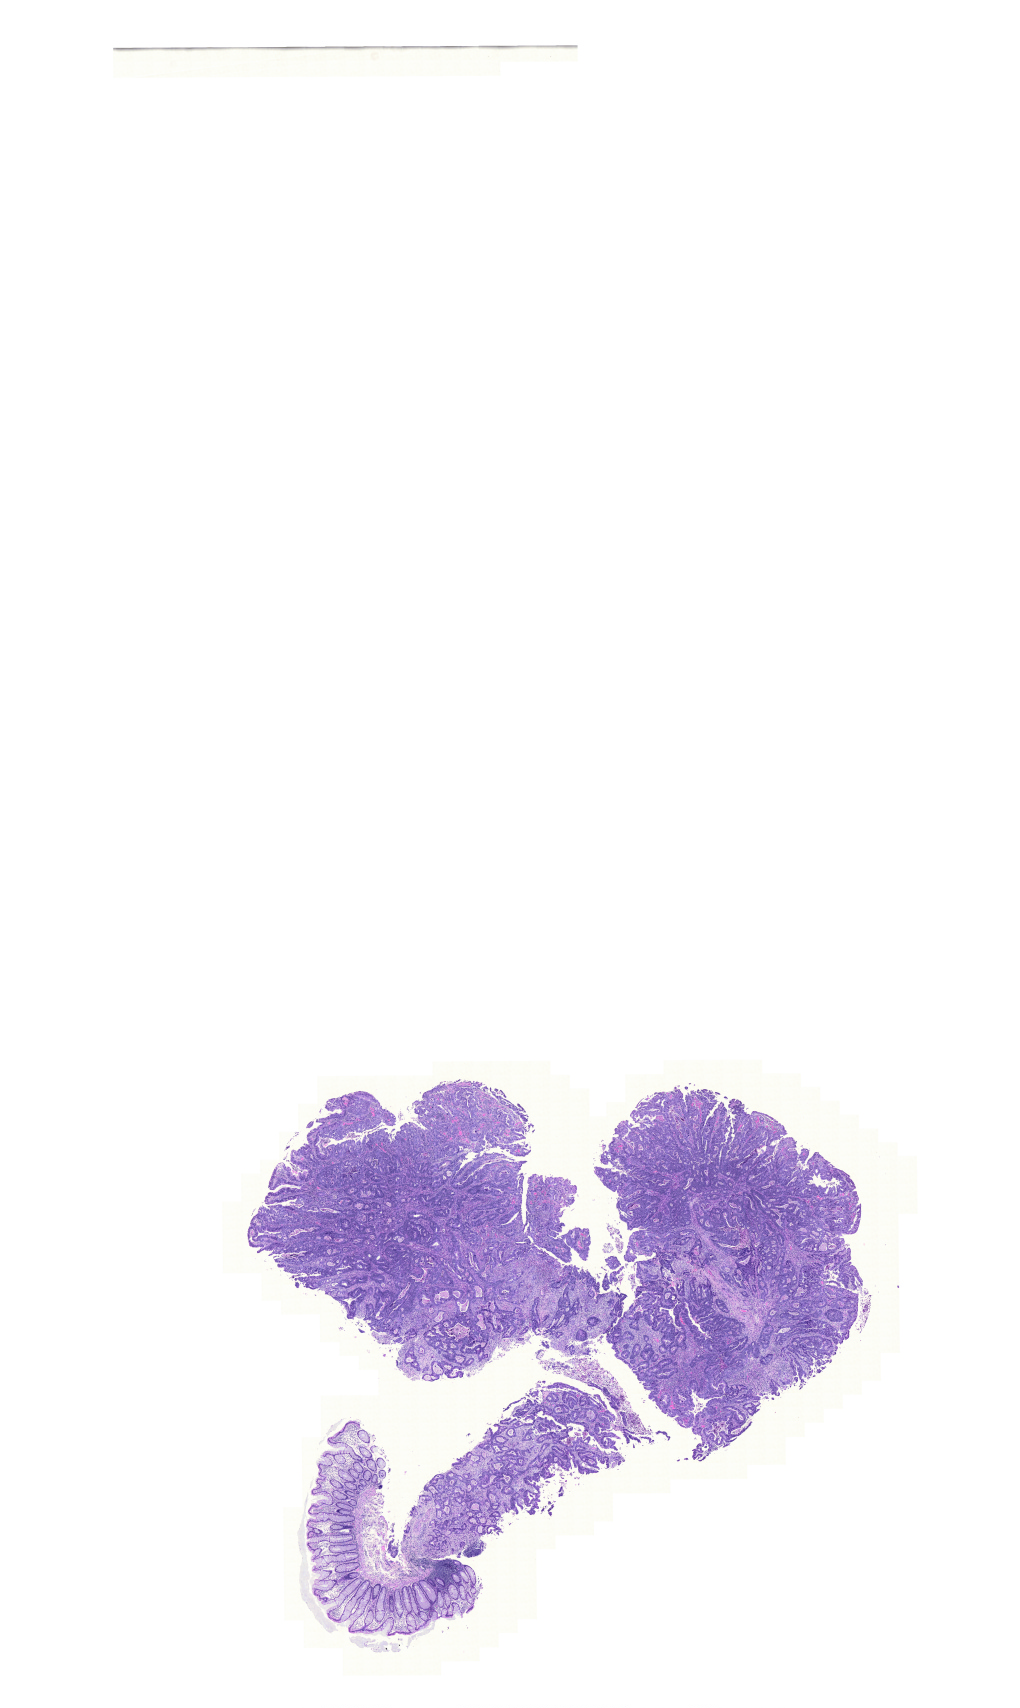
H&E whole-slide image — a low-resolution overview of the entire scanned area, about 15.2 x 25.4 mm (slide scanned at 20x); formalin-fixed paraffin-embedded (FFPE) diagnostic section; primary tumour sample from the rectum. Male patient; age at initial diagnosis 68 years.
- diagnosis: Adenocarcinoma, NOS
- AJCC pathologic stage: IIA (6th edition)